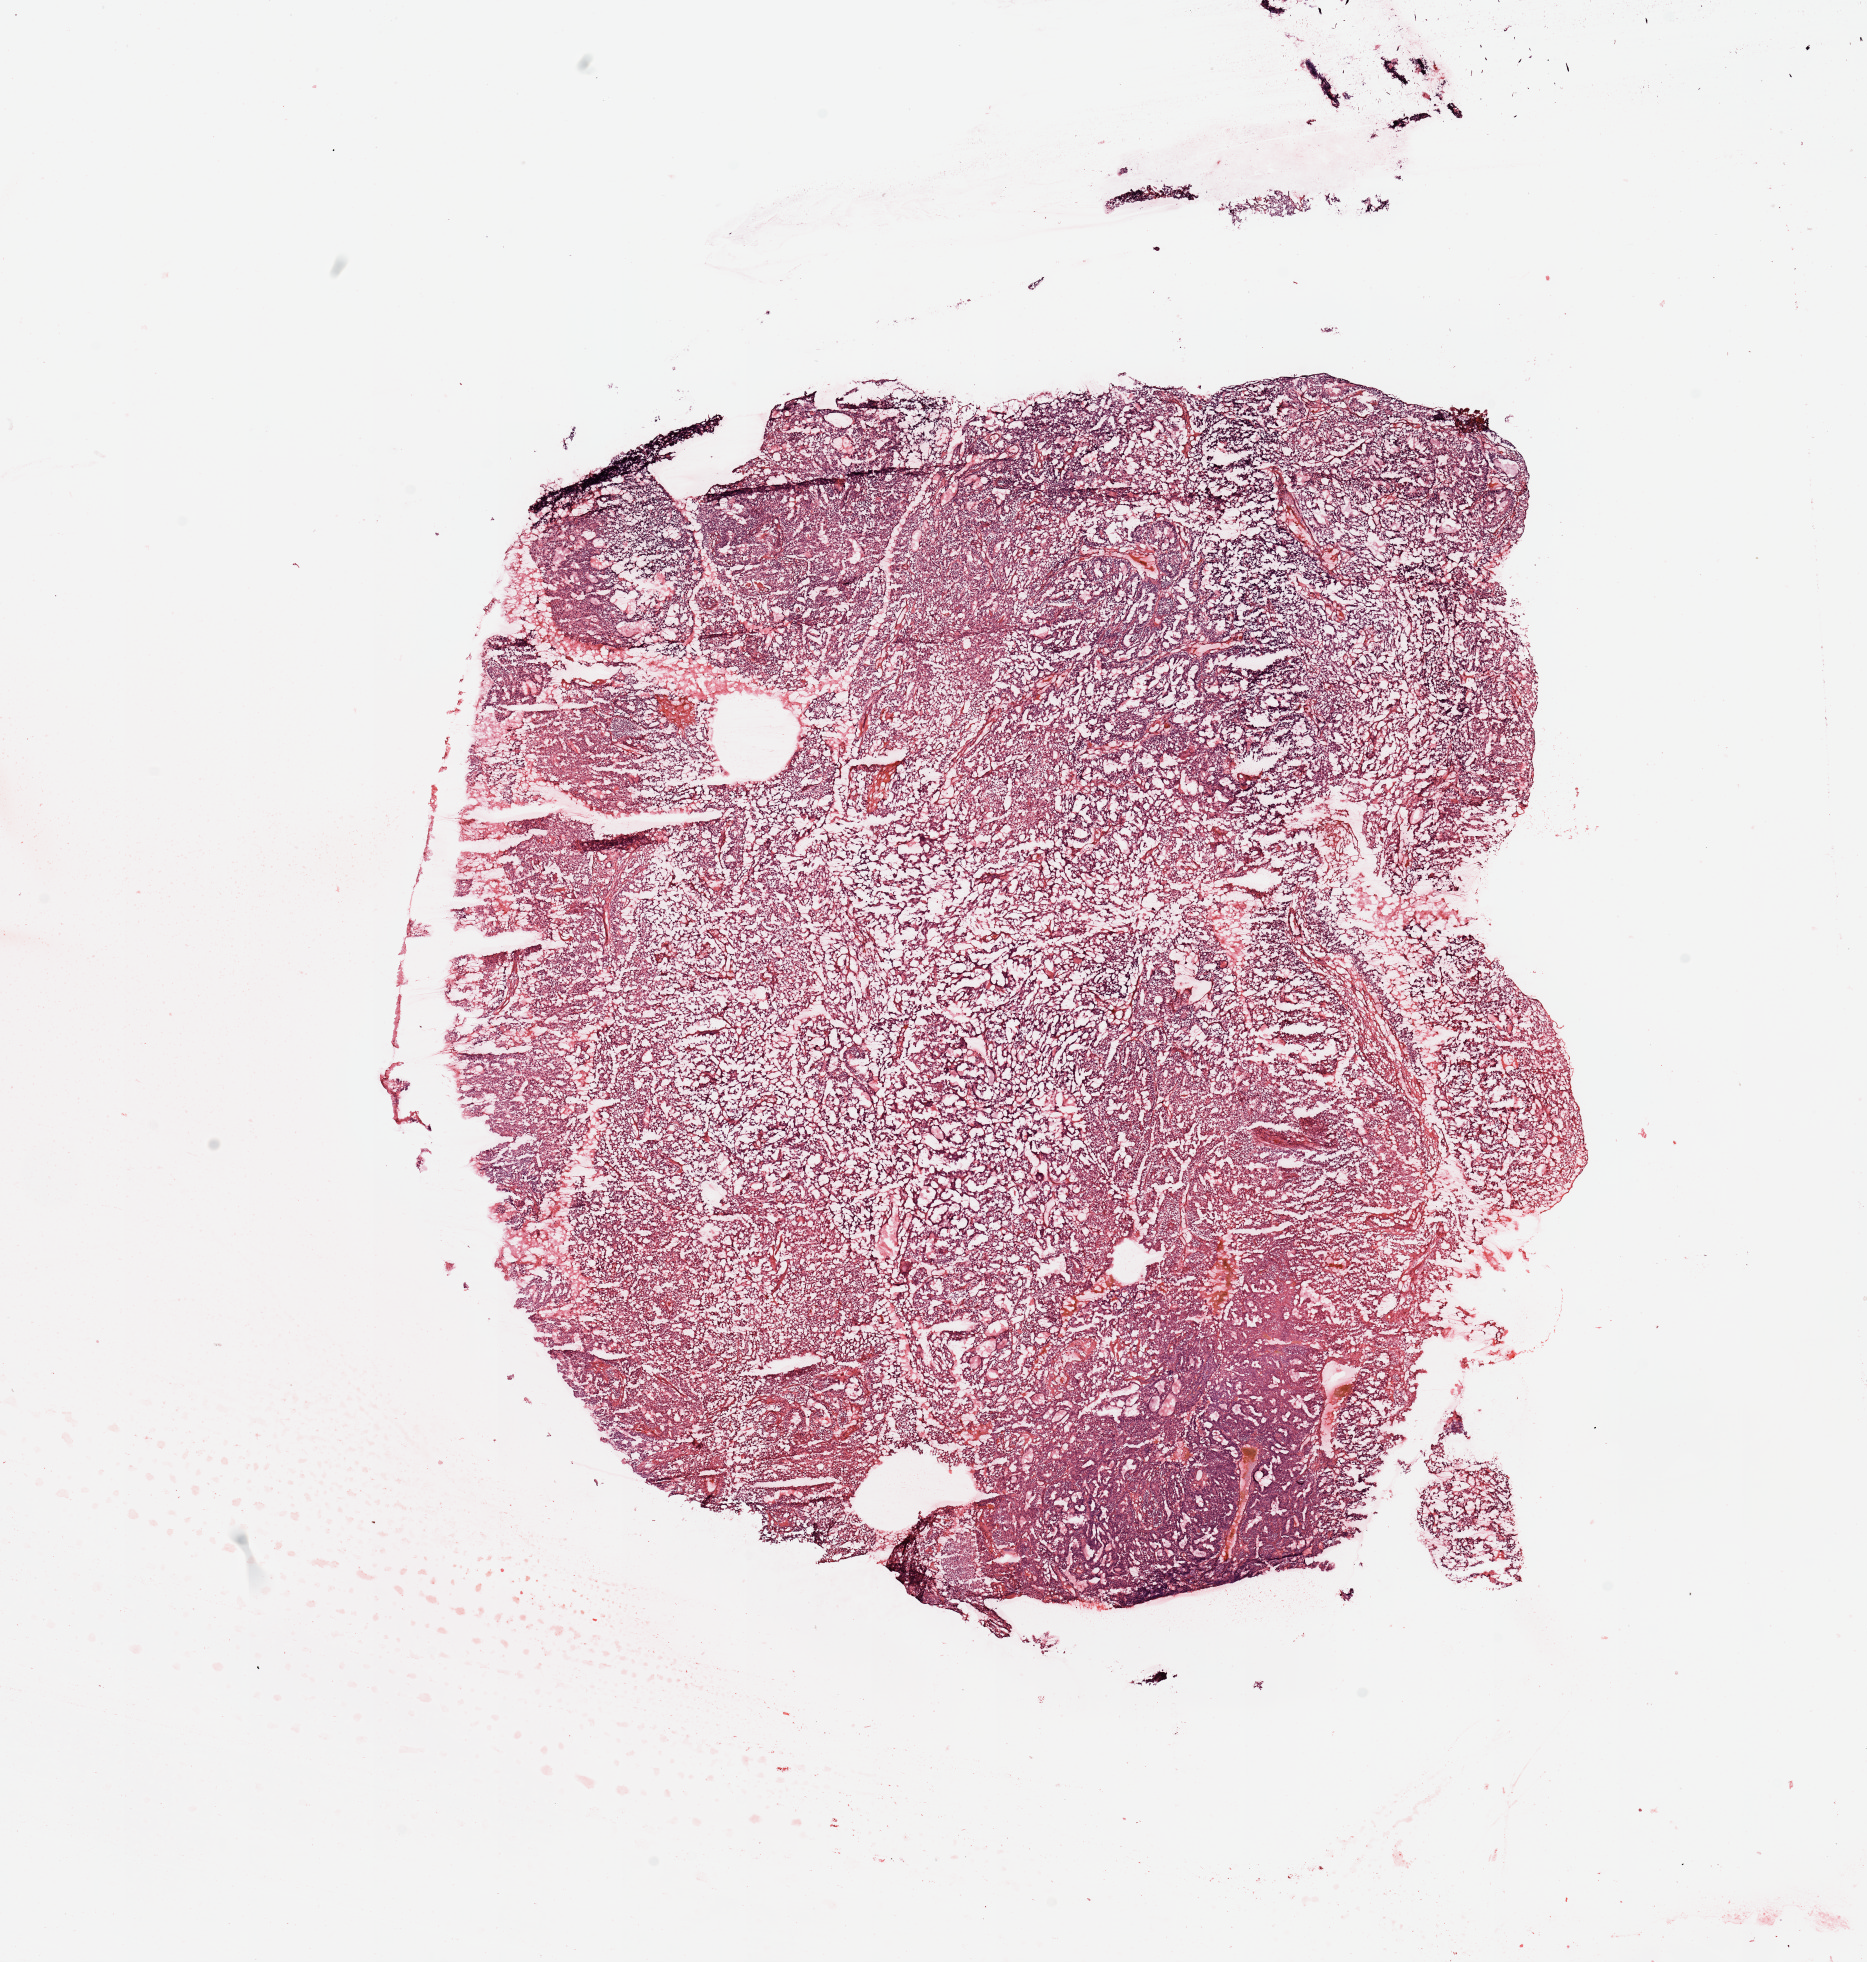
H&E whole-slide image — low-resolution overview of the scanned area, about 14.8 x 15.5 mm (acquisition: 20x scan). Tumour tissue sample, uterus. Patient: female, age 67 years. Histologic grade: G2 (moderately differentiated).
Histologic diagnosis: Endometrioid adenocarcinoma, NOS. AJCC pathologic stage: I.